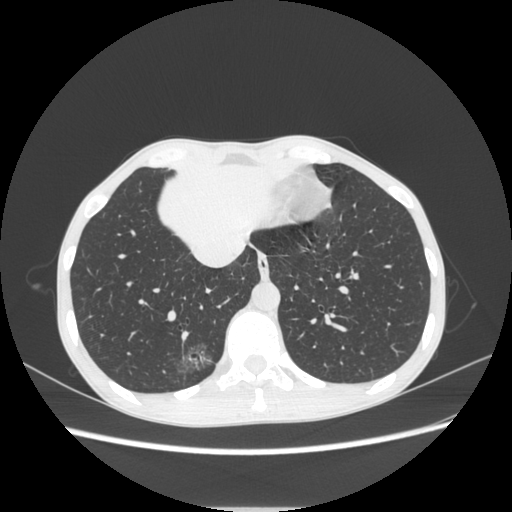
Chest CT, one axial slice. Position 77 of 272 along the scan axis. Reconstruction kernel STANDARD. 120 kVp. Lung window (W 1500 / L -600 HU). 1.25 mm slice thickness. 512 × 512 image matrix, field of view 350 × 350 mm. Female patient, age 51 years. From the clinical record (not read from this slice): clinical TNM (as recorded): T1c N0 M0.
Outlined on this slice (bounding box drawn by a radiologist):
- lung tumour (recorded histology: adenocarcinoma): bounding box [x1, y1, x2, y2] px = [169, 337, 219, 386]